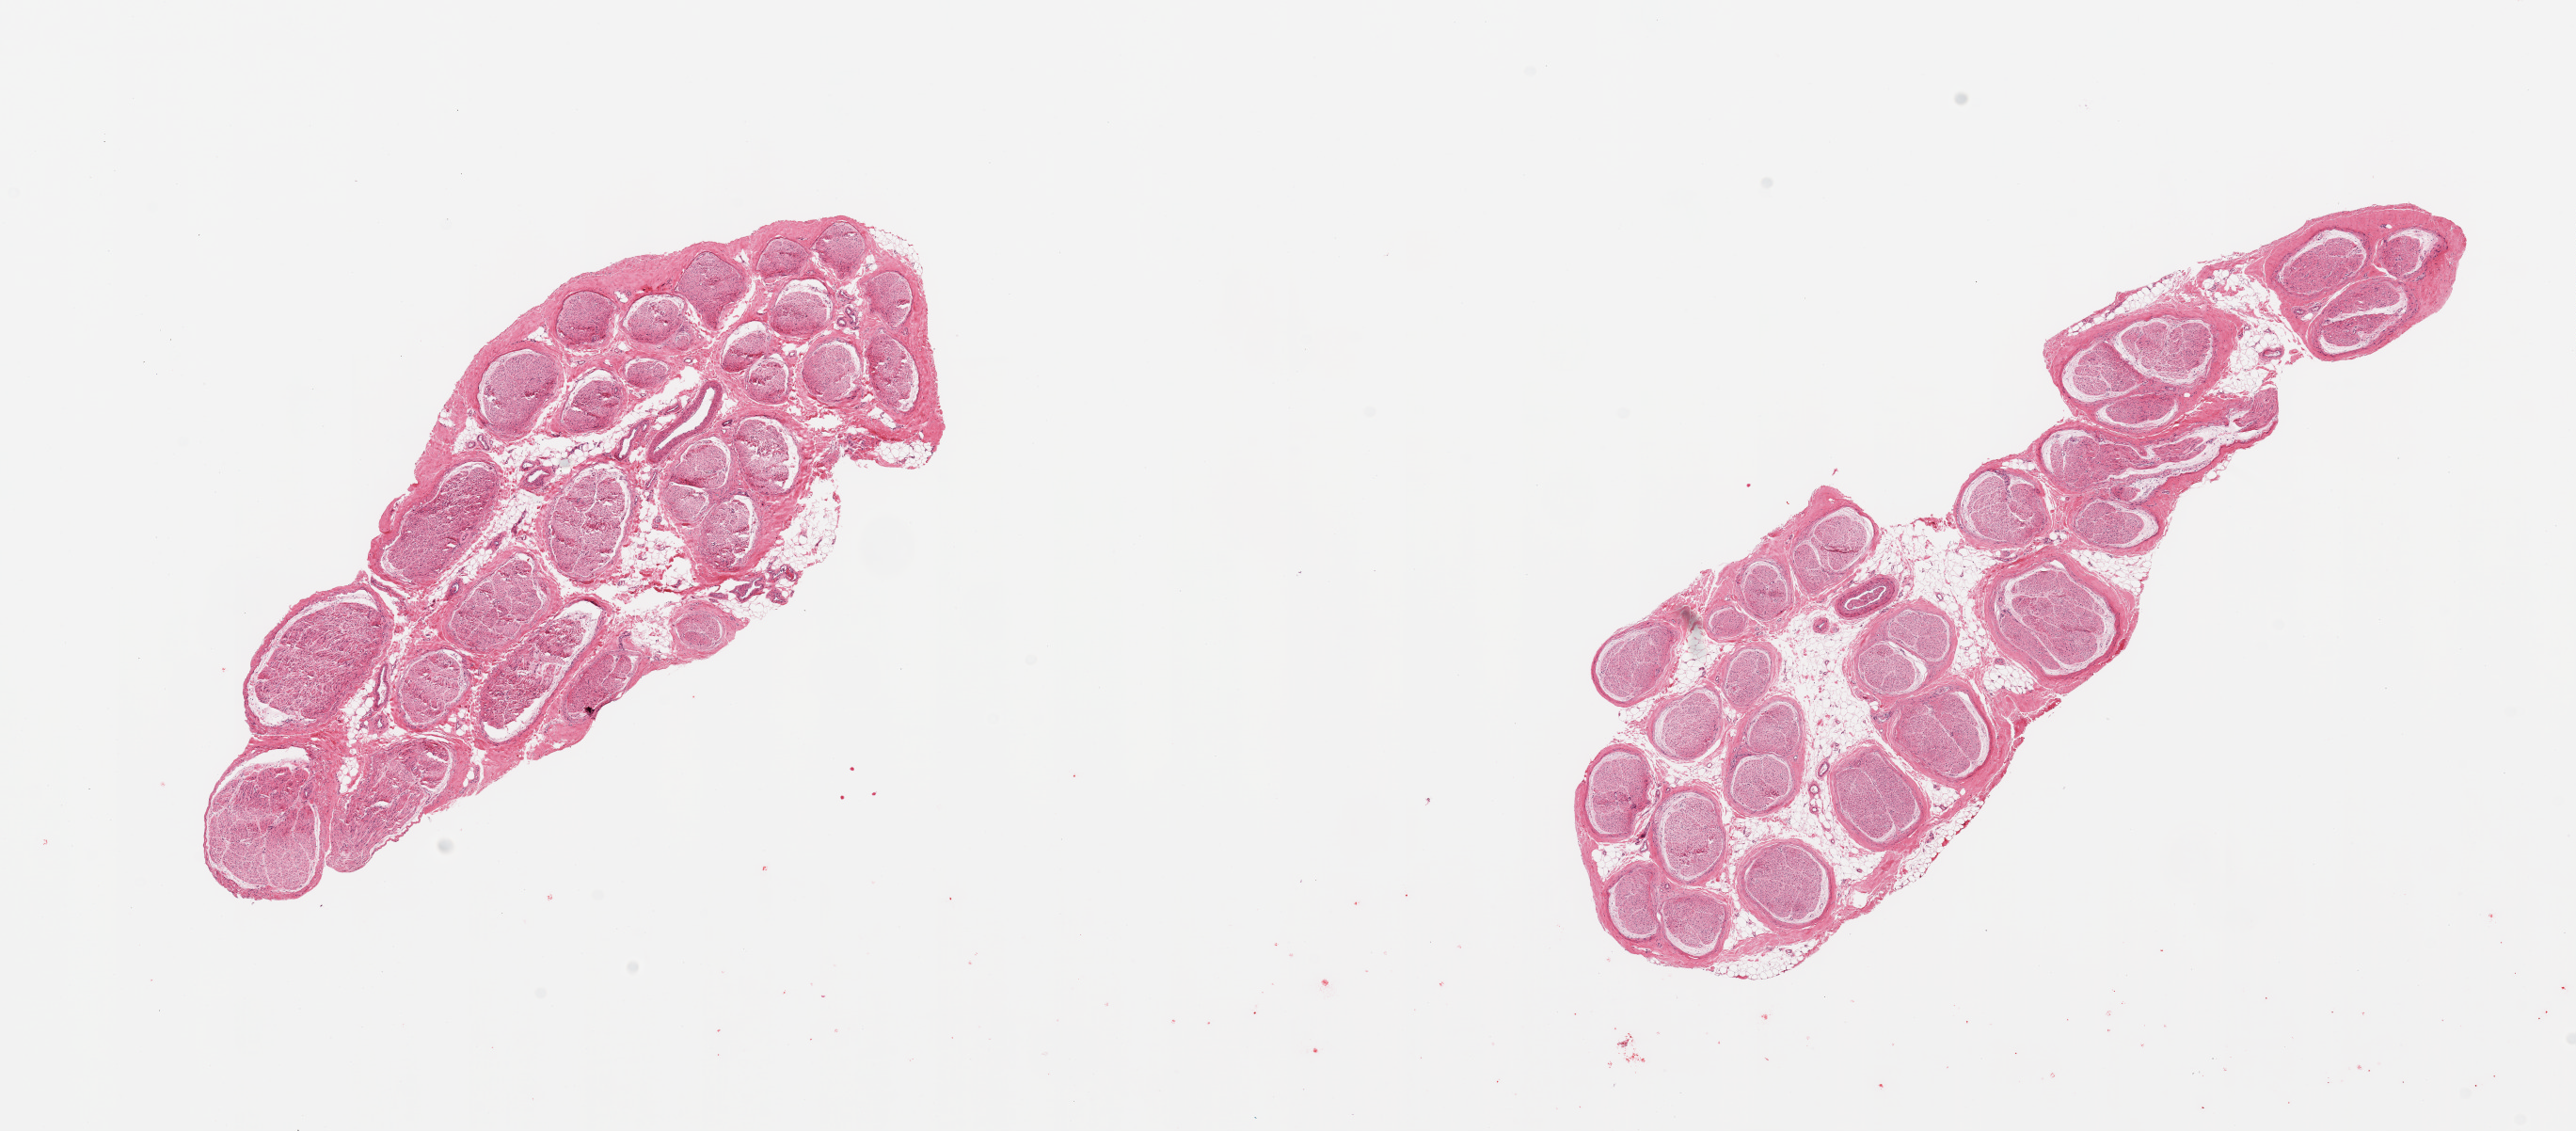
Digitized H&E-stained section — whole scanned area (about 21.7 x 9.5 mm) shown as a low-resolution overview, PAXgene-fixed, paraffin-embedded tissue, target tissue: tibial nerve, donor tissue sample.
* review note (as recorded): 2 pieces; up to 20% predominantly internal fat